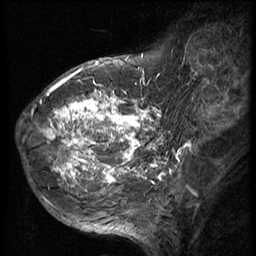
Breast MRI (dynamic contrast-enhanced), one sagittal slice; position 18 of 56 along the scan axis; 3 images stored at this slice position (order not interpretable as contrast timing); 1.5 T; TE 4.2 ms, TR 9 ms; 256 × 256 image matrix. Female patient, age 49 years. Case-level facts recorded for this patient, not image findings: setting: breast cancer imaged before/during neoadjuvant chemotherapy; receptor status: HER2-positive.
Outlined on this slice (semi-automatically segmented with operator editing):
- analysis volume of interest (the breast-tissue region the enhancement analysis was run in; not a lesion): bounding box [x1, y1, x2, y2] px = [37, 85, 147, 207]
- tumour enhancement mask (voxels above the 140 % enhancement threshold inside the analysis volume of interest): [37, 85, 147, 206]